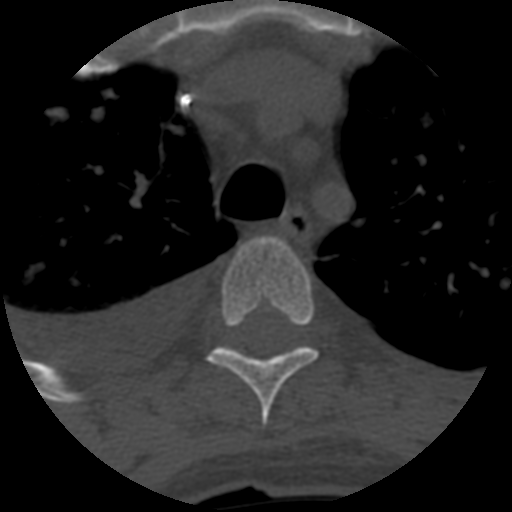
CT including the spine, one axial slice; slice 470 of 708 in the series (ordered by position); one of 3 acquisitions stored at this slice position; bone window (W 1800 / L 400 HU); 1.25 mm slice thickness; 512 × 512 image matrix, field of view 160 × 160 mm. Patient age 55 years. From the clinical record (not read from this slice): primary cancer: colon.
Annotated regions visible in this slice (semi-automatically segmented with operator editing):
- T4 vertebra: bounding box [x1, y1, x2, y2] px = [208, 236, 319, 427]